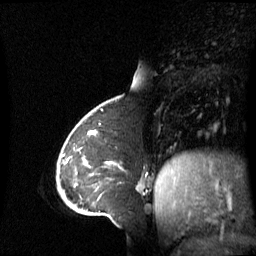
Breast MRI (dynamic contrast-enhanced), one sagittal slice; slice 19 of 60 in the series (ordered by position); dynamic contrast-enhanced series, image 2 of 3 at this slice position (ordered by acquisition); 1.5 T; TE 4.2 ms, TR 8.4 ms; 2.8 mm slice thickness; 256 × 256 image matrix, field of view 270 × 270 mm. Female patient, age 43 years. From the clinical record (not read from this slice): setting: breast cancer imaged before/during neoadjuvant chemotherapy; receptor status: triple-negative.
Outlined on this slice (semi-automatically segmented with operator editing):
- analysis volume of interest (the breast-tissue region the enhancement analysis was run in; not a lesion): box from (x=69, y=137) to (x=143, y=198) px
- tumour enhancement mask (voxels above the 70 % enhancement threshold inside the analysis volume of interest): (x=69, y=150)–(x=110, y=164)